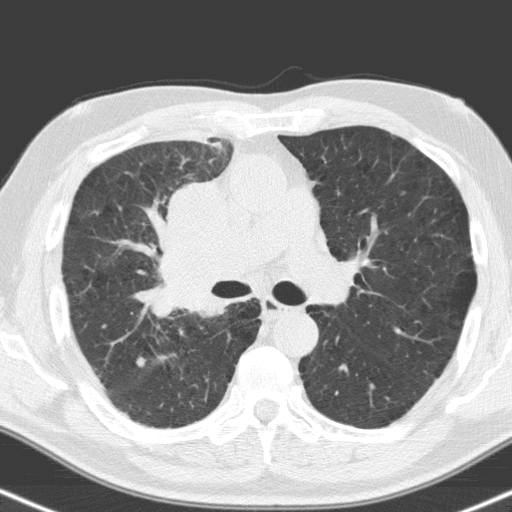
Low-dose screening chest CT, one axial slice. Lung window (W 1500 / L -600 HU). 512 × 512 image matrix, field of view 324 × 324 mm.
Structures marked on this image (outlined manually by an expert reader):
- lesion 1 (tumor, hilum of right lung): bounding box <159,184,255,314> (left, top, right, bottom; pixels)